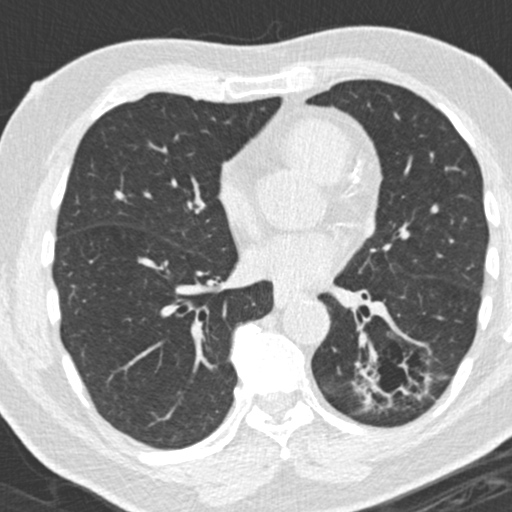
Chest CT (low-dose screening protocol), one axial image, third annual screen, lung window (W 1500 / L -600 HU), slice 91 of 180 in the series. Male participant, aged 66 years at enrolment. Former smoker at enrolment.
Expert reader's lesion annotation, box from (x=356, y=348) to (x=427, y=428) px. The exam's reader record, not a measurement of the box and not confirmed to be the same lesion: non-calcified nodule or mass ≥4 mm, left lower lobe, 31 × 24 mm, spiculated (stellate) margins, pre-existing on the prior screen: yes; interval growth: yes.